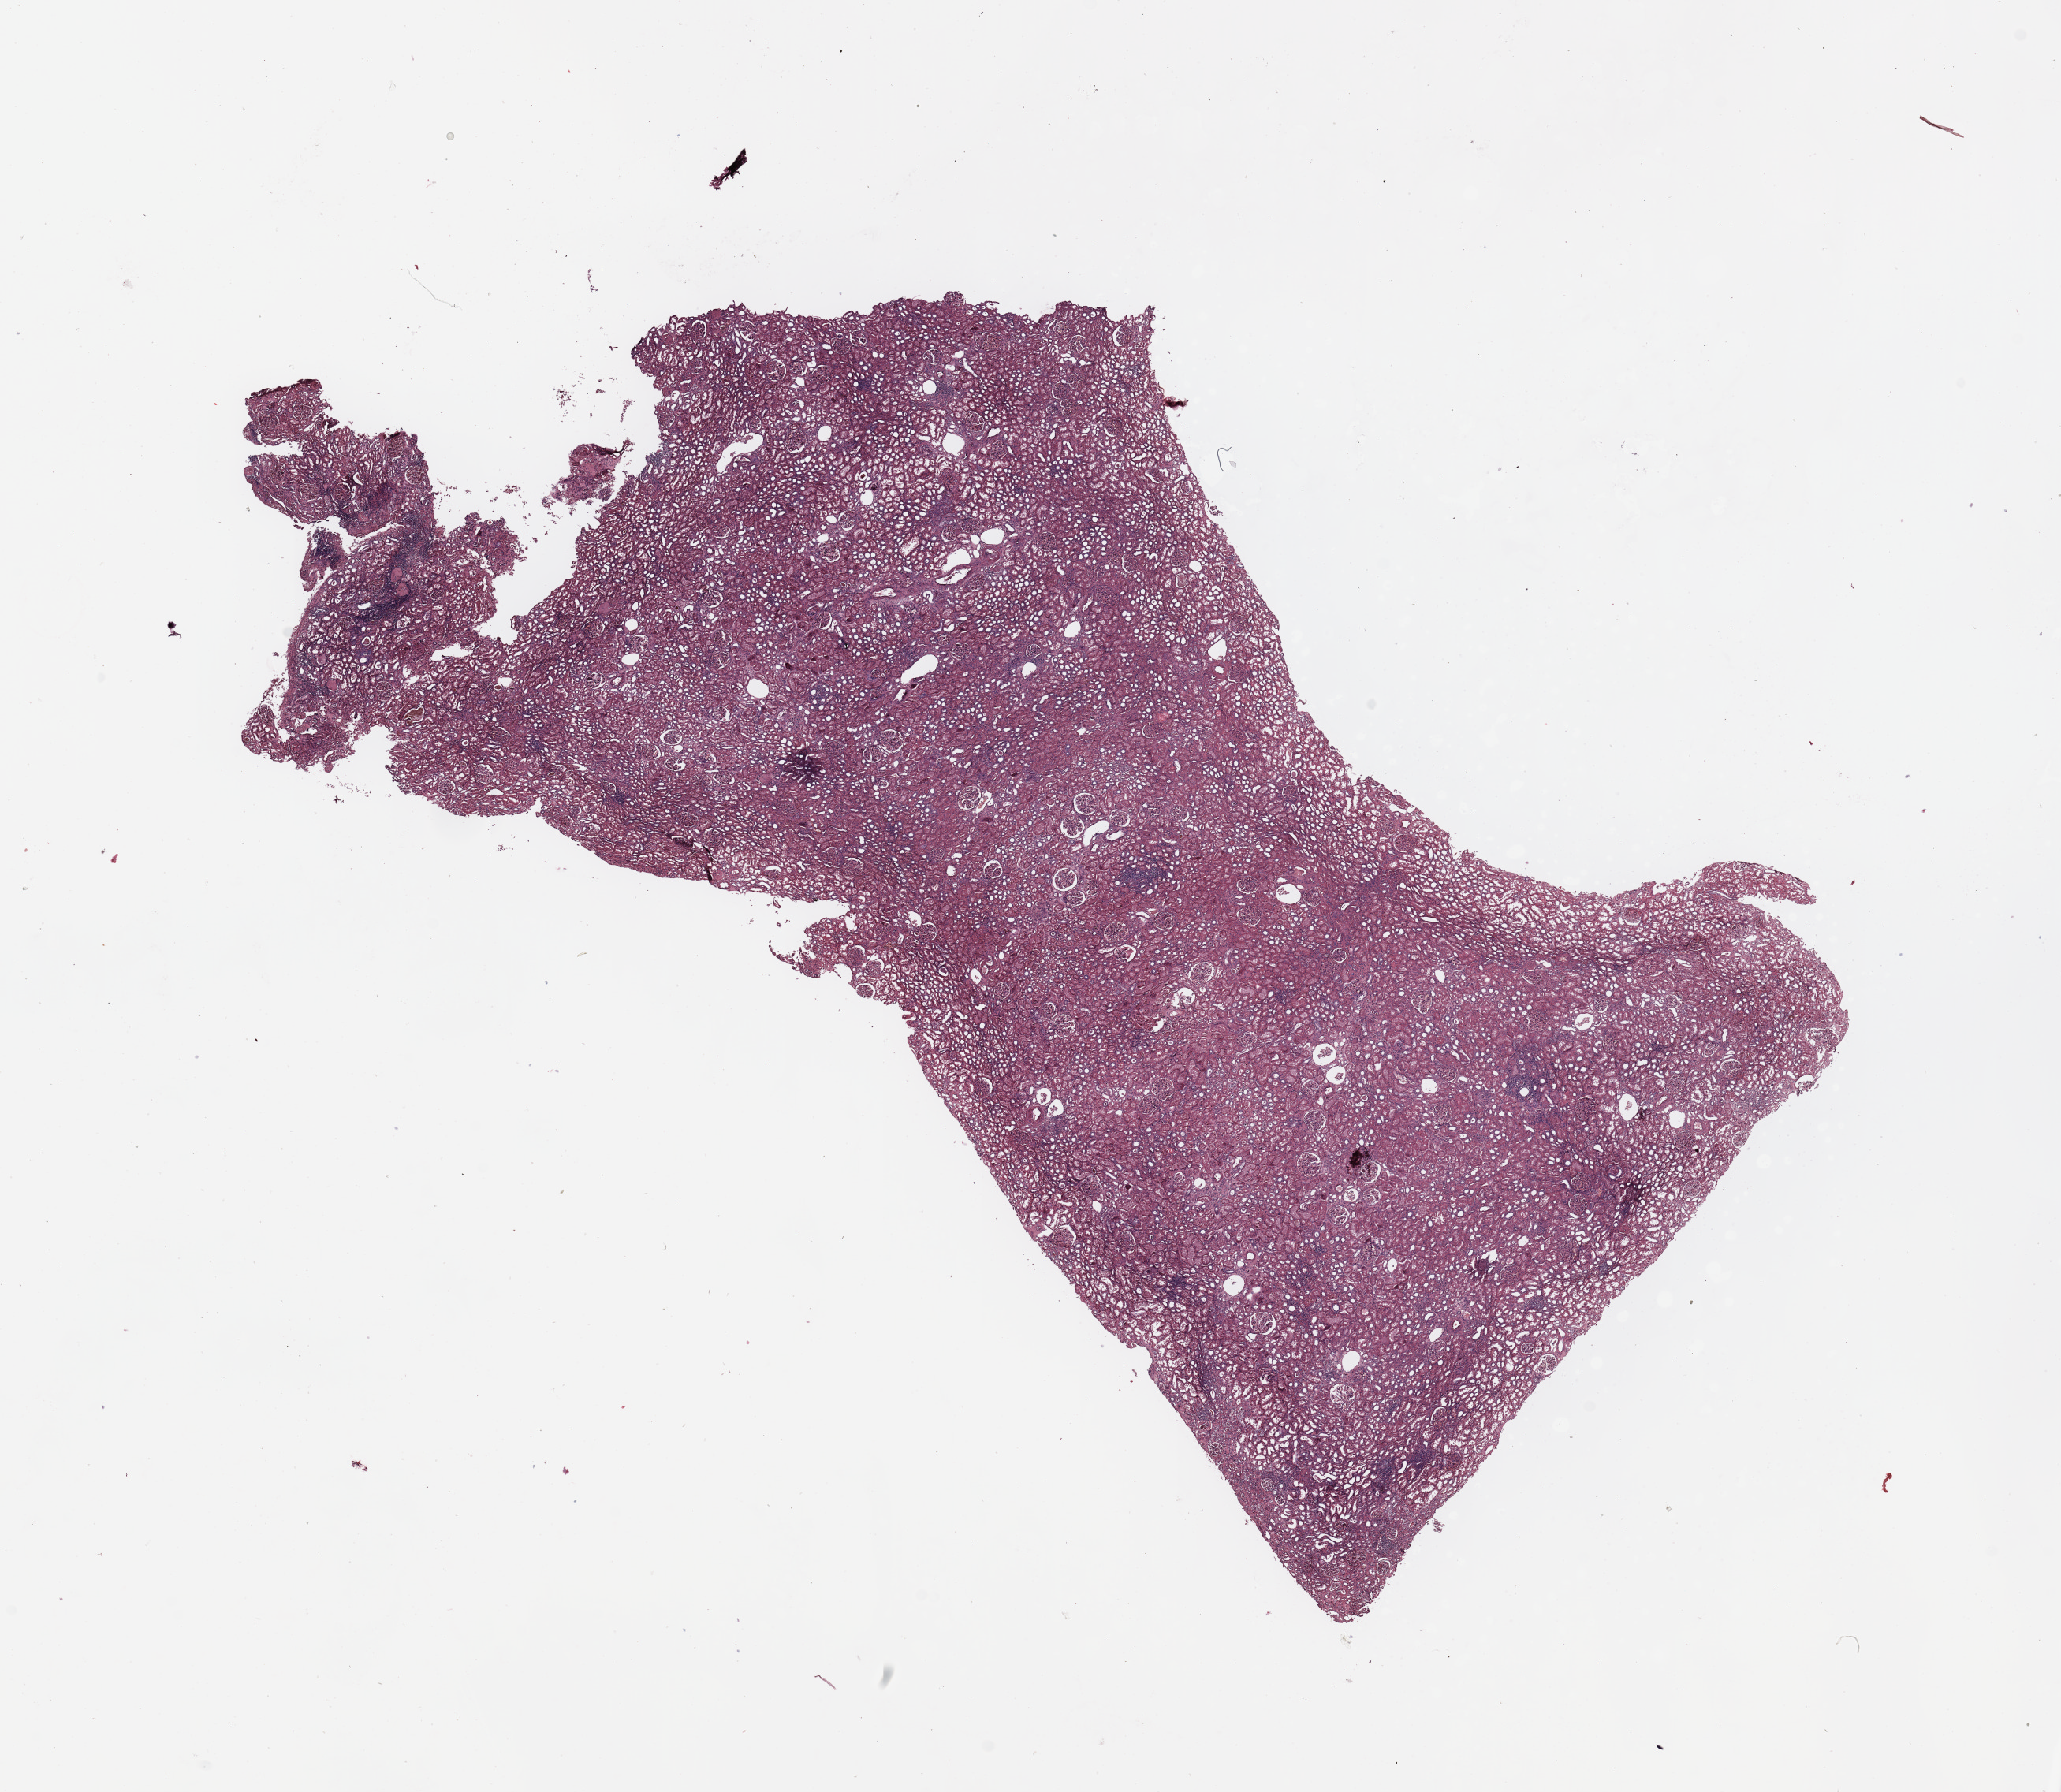
Digitized H&E tissue section (whole slide), whole scanned area (about 20.7 x 18.0 mm, slide scanned at 20x) shown as a low-resolution overview, normal (non-tumour) tissue sample, sampled site: kidney. 60-year-old male patient.
• this section: normal (non-tumour) tissue from the same patient
• patient diagnosis: Renal cell carcinoma, NOS